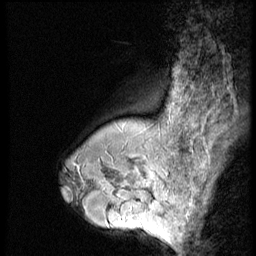
Breast MRI (dynamic contrast-enhanced), one sagittal slice; 3 images stored at this slice position (order not interpretable as contrast timing); 1.5 T; TE 4.2 ms, TR 9 ms; 2.5 mm slice thickness; 256 × 256 image matrix. Female patient, age 43 years. From the clinical record (not read from this slice): setting: breast cancer imaged before/during neoadjuvant chemotherapy; receptor status: HR-positive, HER2-negative.
Outlined on this slice (semi-automatically segmented with operator editing):
- analysis volume of interest (the breast-tissue region the enhancement analysis was run in; not a lesion): box from (x=120, y=160) to (x=163, y=207) px
- tumour enhancement mask (voxels above the 140 % enhancement threshold inside the analysis volume of interest): (x=135, y=178)–(x=153, y=187)